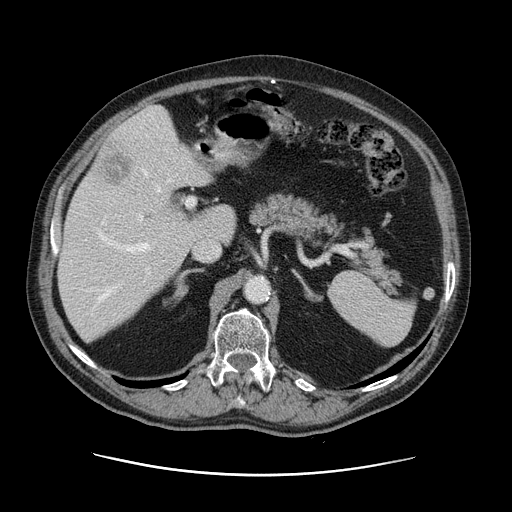
Contrast-enhanced abdominal CT, one axial slice; position 77 of 141 along the scan axis; 120 kVp; intravenous contrast given; soft-tissue window (W 400 / L 40 HU); 512 × 512 image matrix, field of view 395 × 395 mm. Male patient, age 72 years. From the clinical record (not read from this slice): diagnosis: colorectal cancer liver metastases, imaged before liver resection; multiple liver metastases: yes; largest metastasis: 5.4 cm; chemotherapy before resection: yes.
Outlined on this slice (manually delineated by an expert):
- hepatic veins: bounding box [x1, y1, x2, y2] px = [98, 169, 171, 302]
- liver: [58, 107, 236, 341]
- planned liver remnant (the part of the liver to remain after resection): [58, 160, 236, 341]
- portal vein (with intrahepatic branches): [98, 197, 195, 293]
- liver metastasis: [105, 152, 133, 187]